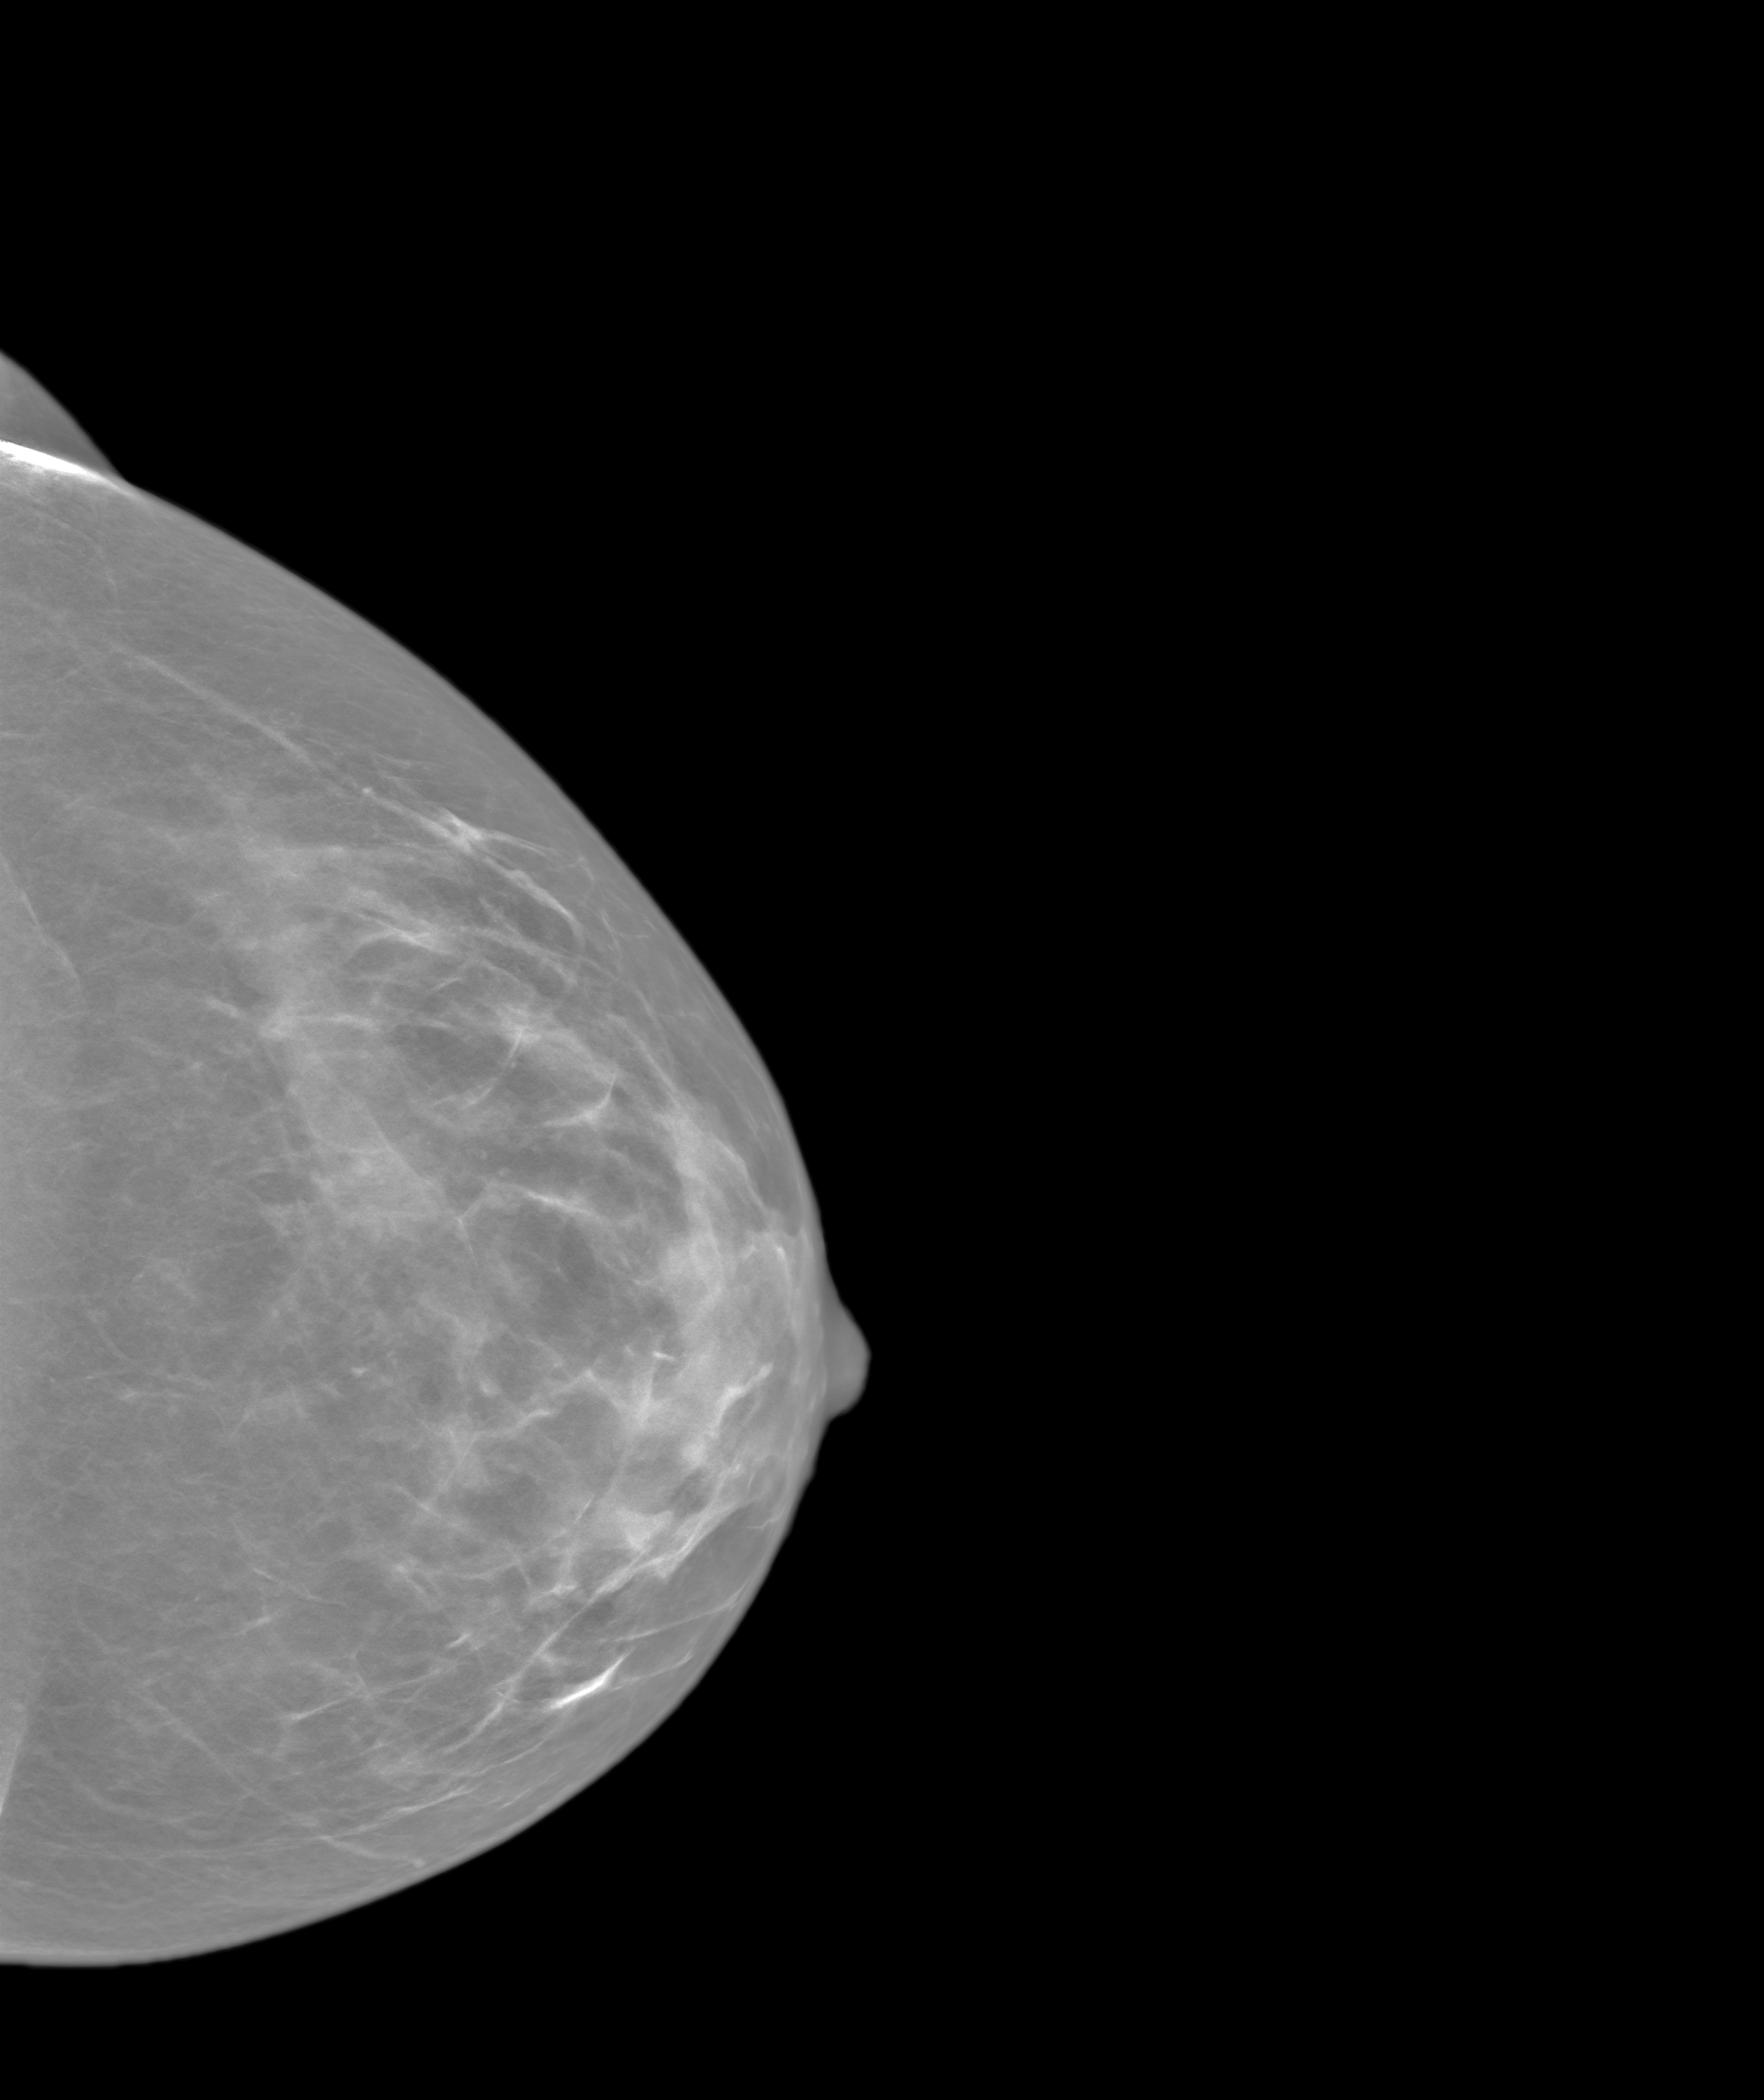
Annual screening mammography examination. Patient: female, 47 years.
Image type: synthesized 2-D view from tomosynthesis. Breast: left. Projection: cranio-caudal projection.